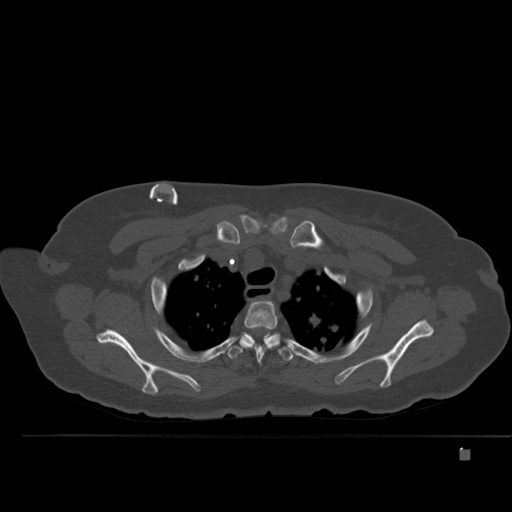
CT including the spine, one axial slice. Slice 387 of 477 in the series (ordered by position). Bone window (W 1800 / L 400 HU). 1.5 mm slice thickness. 512 × 512 image matrix. Patient: female, 74 years. From the clinical record (not read from this slice): primary cancer: colon.
Outlined on this slice (semi-automatic segmentation, software-assisted and operator-edited):
- T1 vertebra: bounding box (x1, y1, x2, y2) in pixels: (264, 301, 271, 302)
- T2 vertebra: (239, 301, 278, 362)
- T3 vertebra: (227, 332, 293, 361)